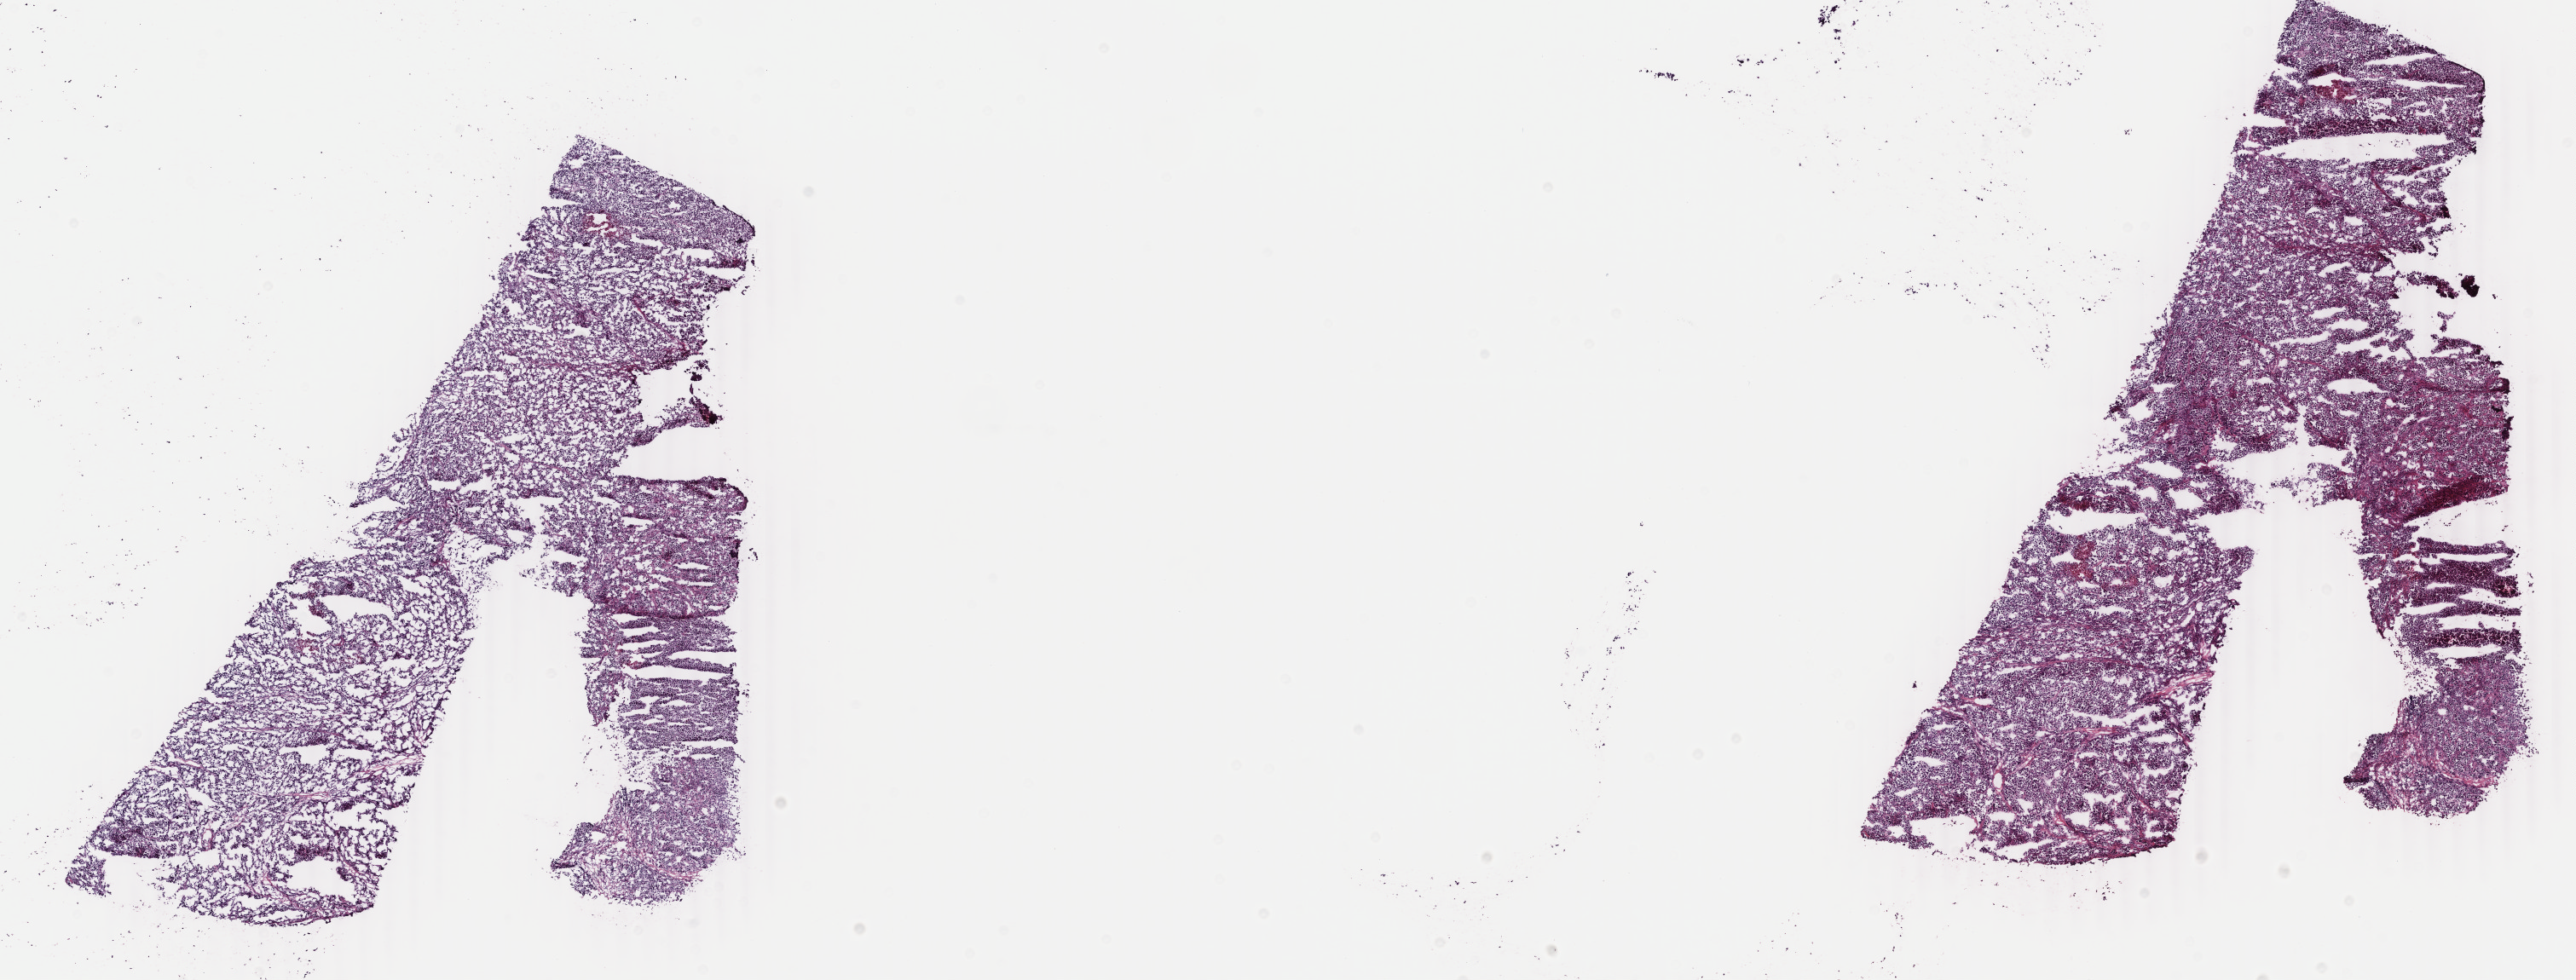
Digitized Hematoxylin and eosin (H&E) stained tissue section (whole slide), a low-resolution overview of the entire scanned area, about 24.0 x 9.1 mm, frozen section from the top of the tissue portion, metastatic tumour sample, sampled site not recorded. Patient: male, age at initial diagnosis 37 years. Slide review estimates, as recorded: tumour cells 90%, tumour nuclei 90%, normal cells 0%, stromal cells 9%, necrosis 1%. Infiltration values recorded for this section: lymphocyte infiltration 2%, monocyte infiltration 1%, neutrophil infiltration 1%.
• this section: metastatic tumour tissue
• patient diagnosis: Malignant melanoma, NOS